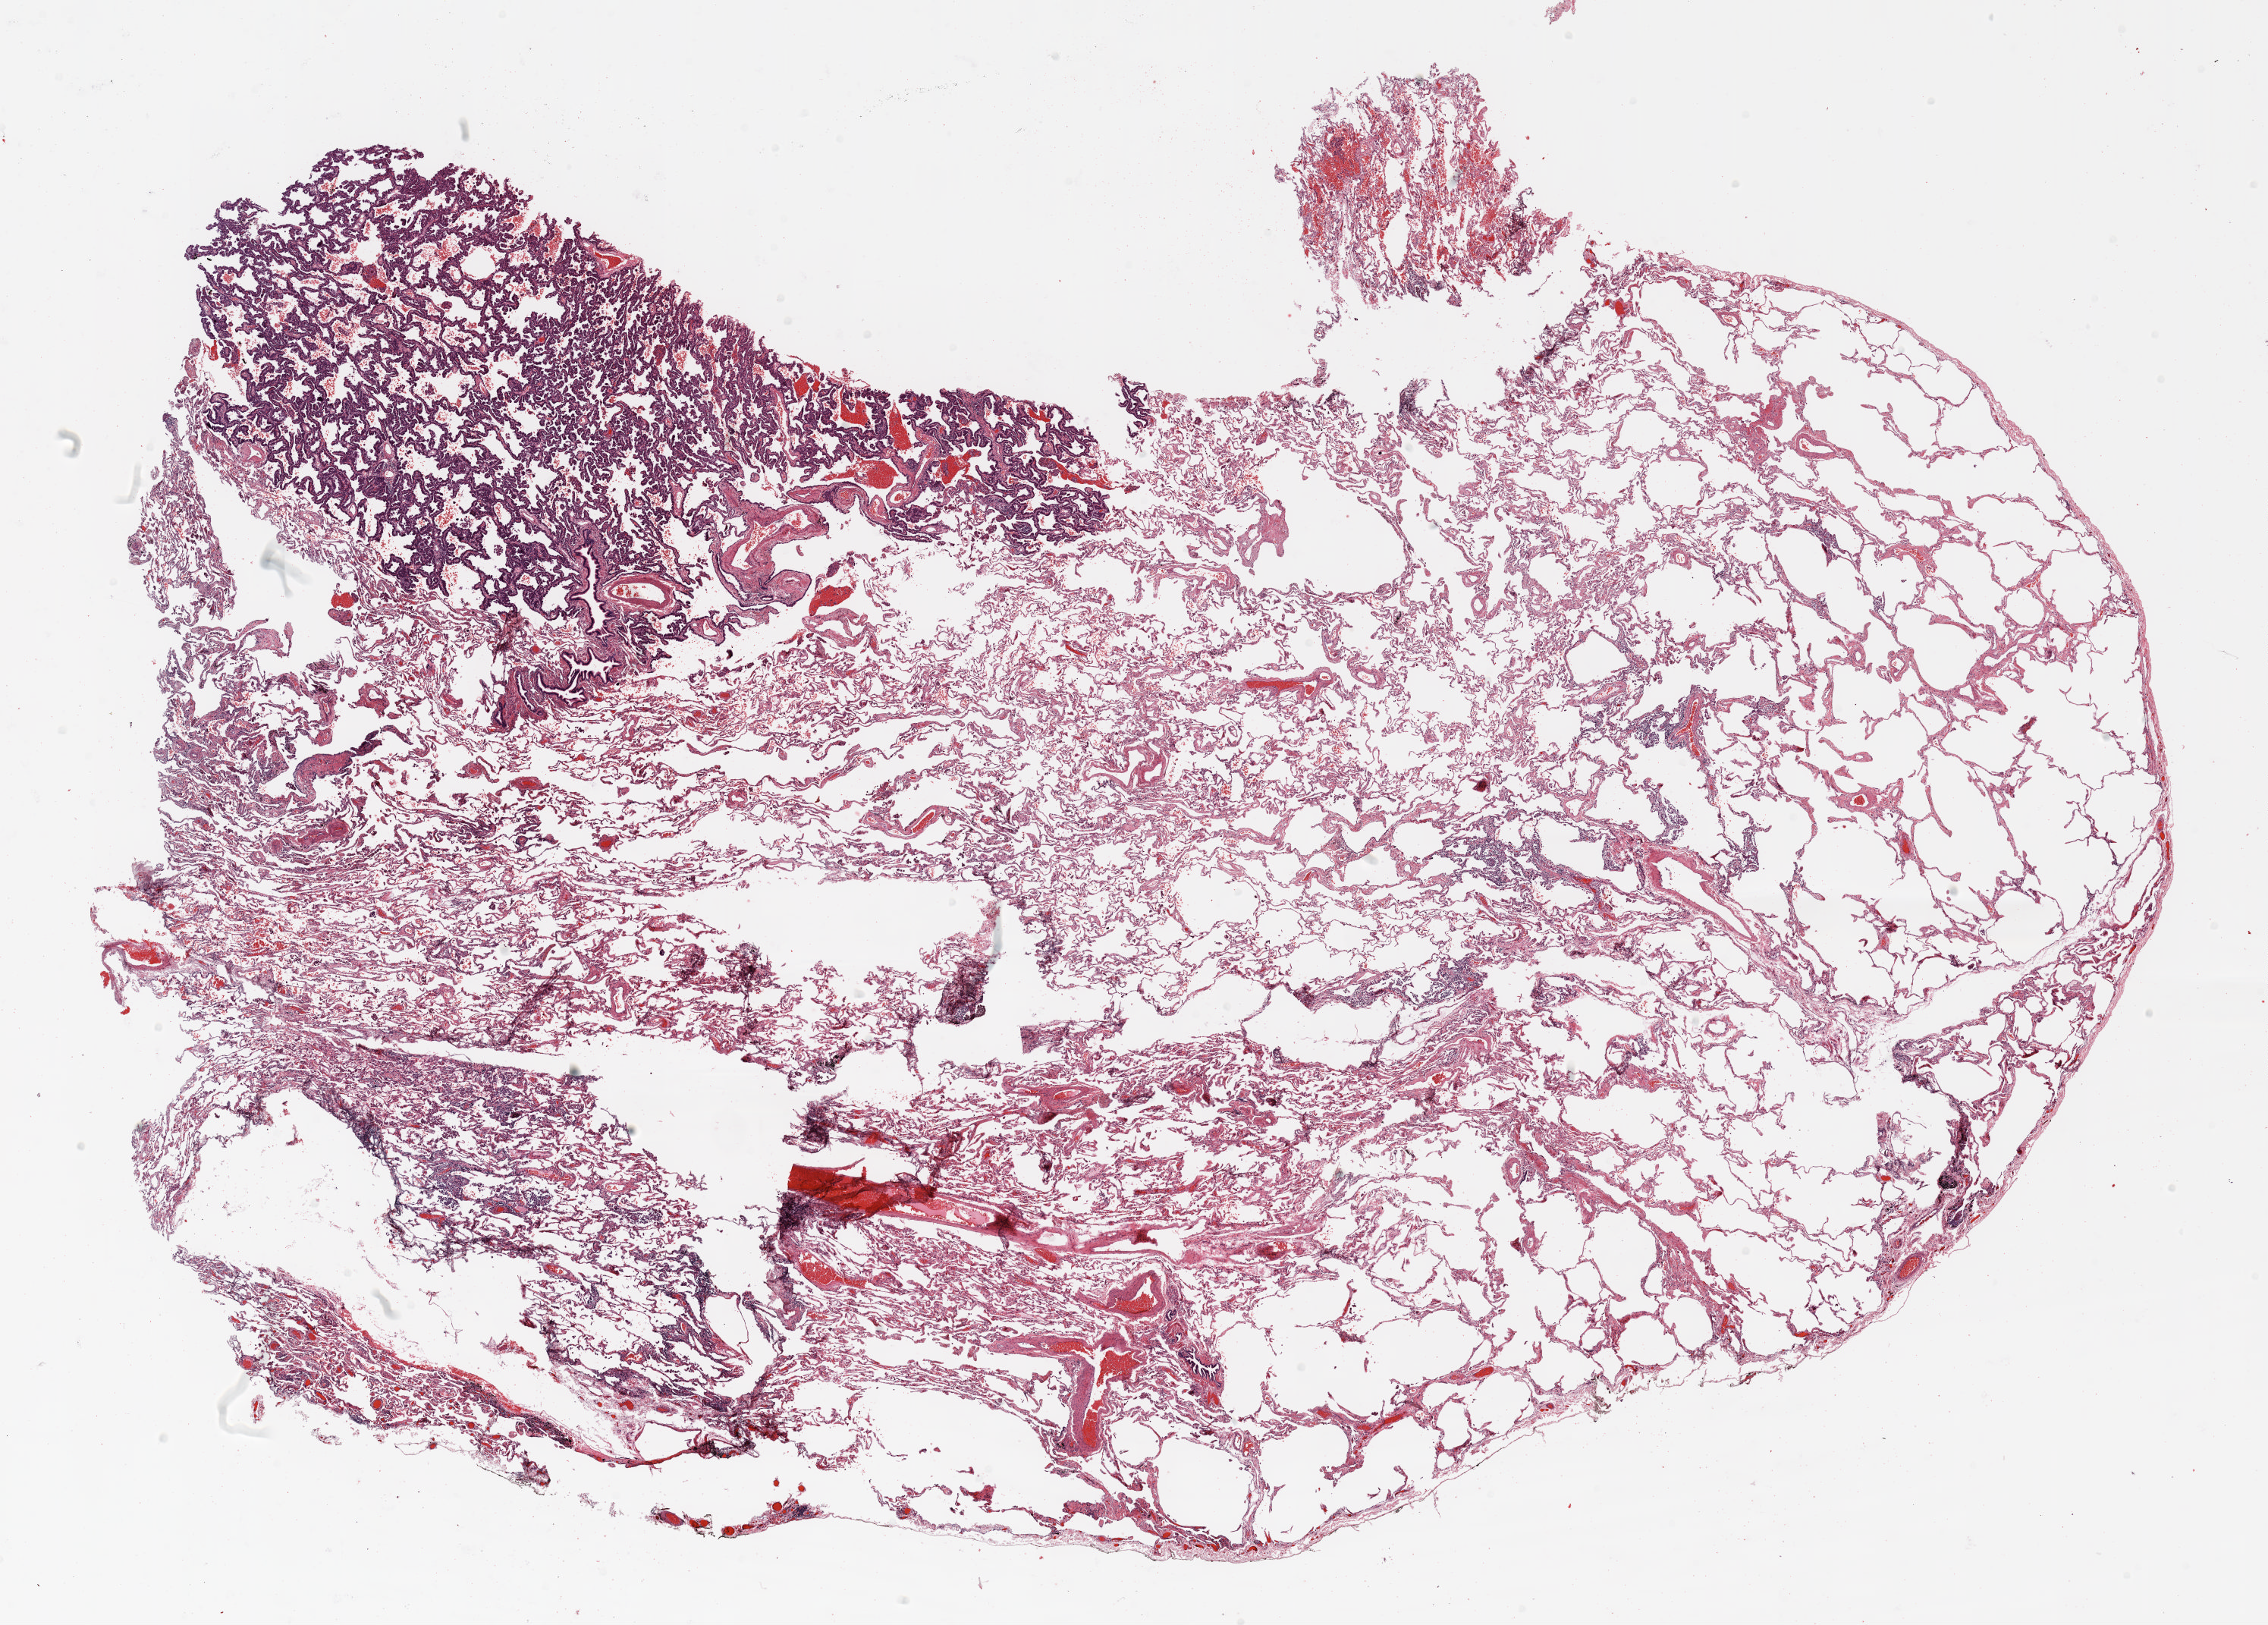
H&E whole-slide image, shown as a low-resolution overview of the whole scanned area (about 24.0 x 17.2 mm, slide scanned at 20x); formalin-fixed paraffin-embedded (FFPE) section; lung tissue. Male patient, aged 59 at enrolment. Former smoker at enrolment.
Participant's lung-cancer diagnosis: Bronchiolo-alveolar carcinoma, non-mucinous.